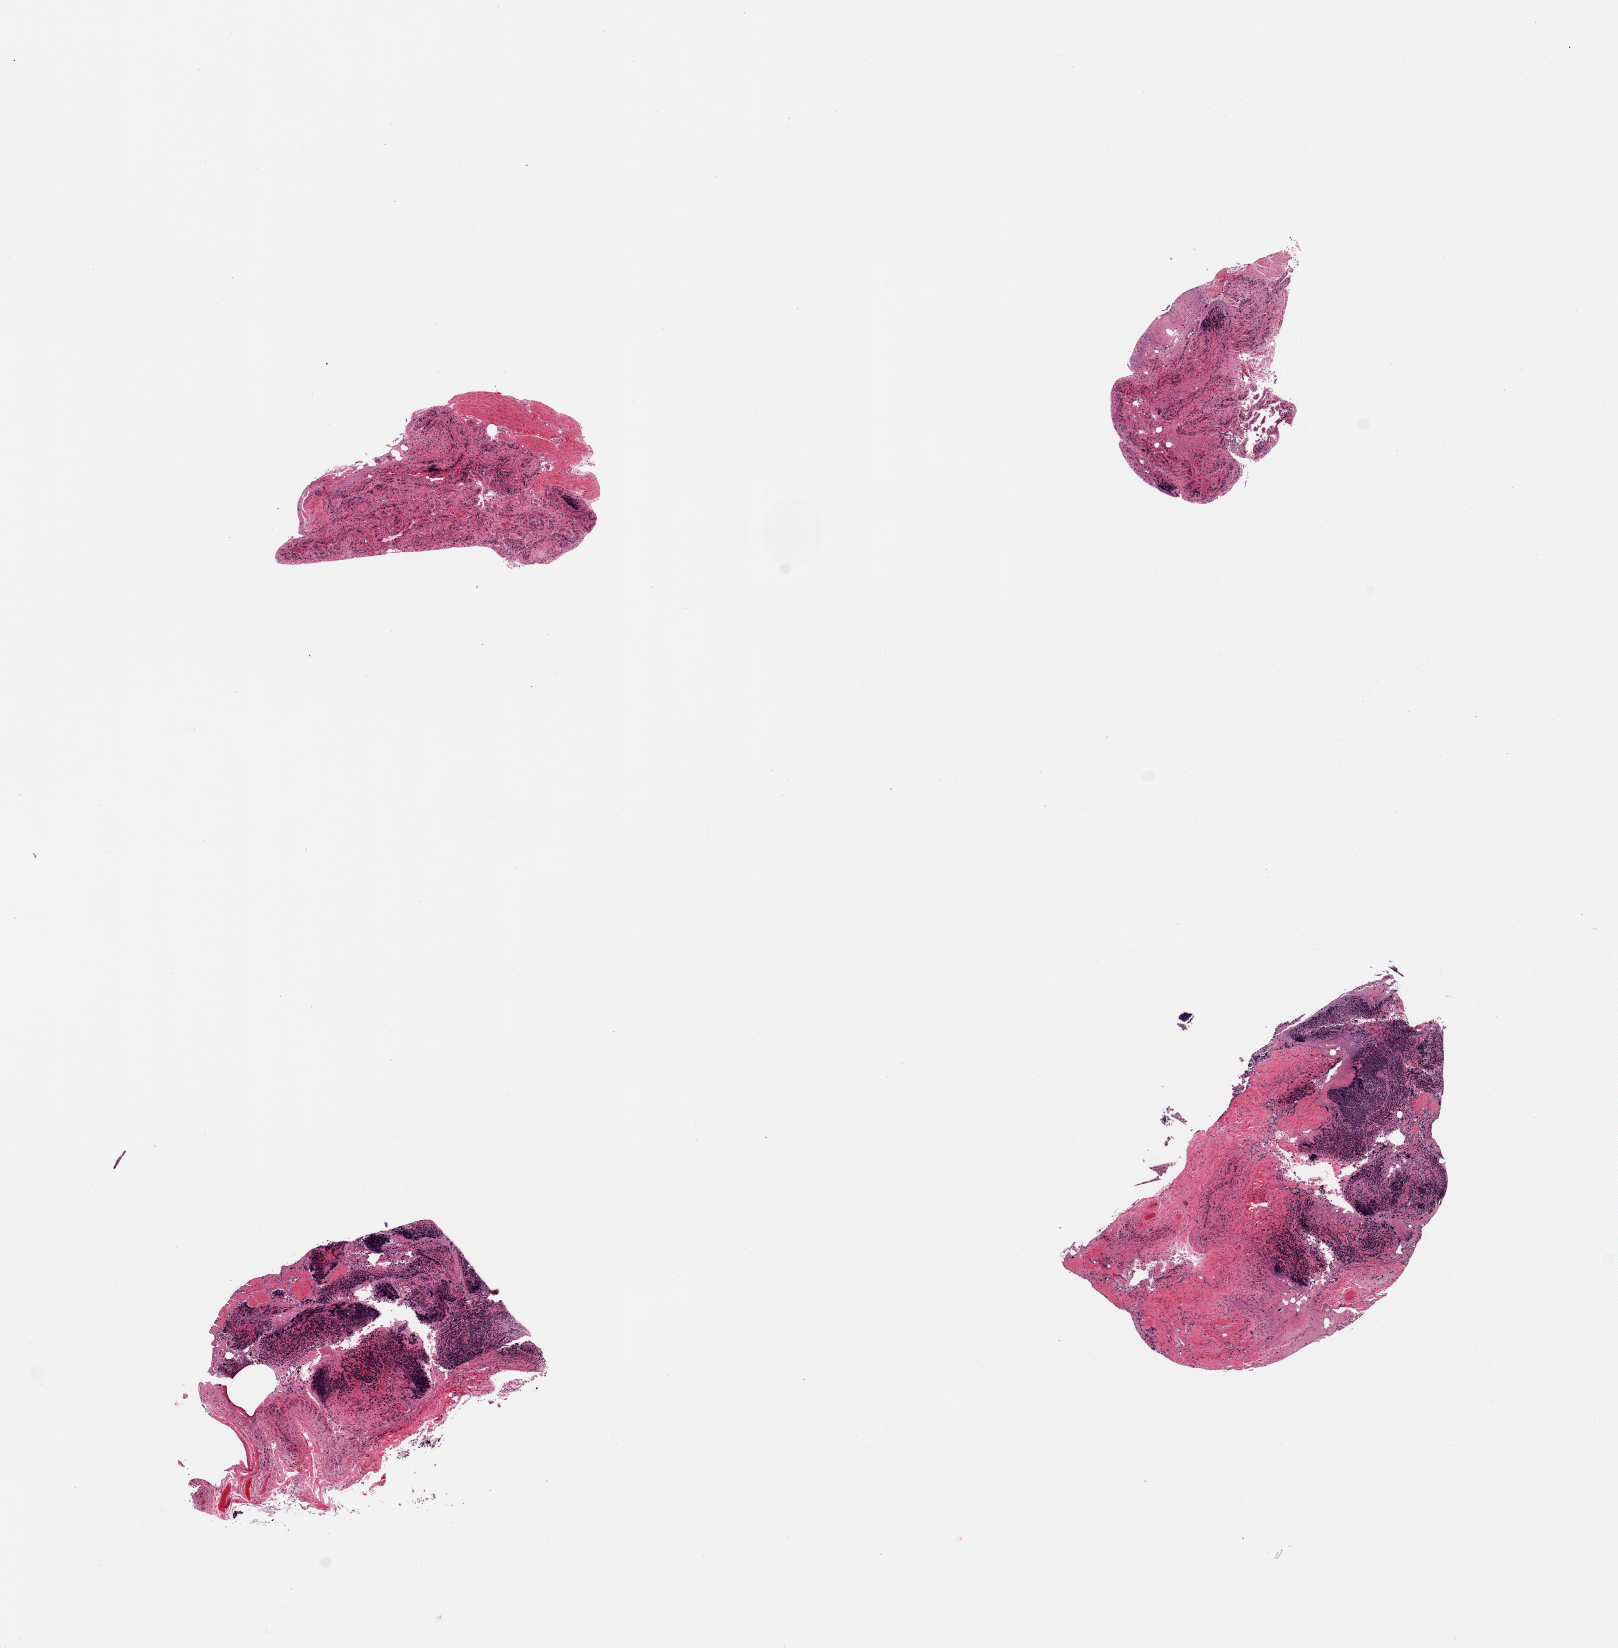
Whole-slide image, H&E stain — whole scanned area (about 12.8 x 13.0 mm) shown as a low-resolution overview, PAXgene-fixed, paraffin-embedded tissue, target tissue: ileum, donor tissue sample. Donor: female.
Review note (as recorded): 4 pieces, target lymphoid aggregates are ~30% total.